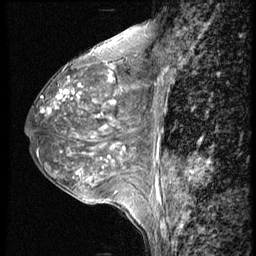
Breast MRI (dynamic contrast-enhanced), one sagittal slice; slice 22 of 56 in the series (ordered by position); 4 images stored at this slice position (order not interpretable as contrast timing); 1.5 T; TE 4.2 ms, TR 9 ms; 2.5 mm slice thickness; 256 × 256 image matrix, field of view 180 × 180 mm. Patient: female, 50 years. Case-level facts recorded for this patient, not image findings: setting: breast cancer imaged before/during neoadjuvant chemotherapy; receptor status: triple-negative.
Structures marked on this image (semi-automatic segmentation, software-assisted and operator-edited):
- analysis volume of interest (the breast-tissue region the enhancement analysis was run in; not a lesion): bounding box (x1, y1, x2, y2) in pixels: (24, 46, 148, 188)
- tumour enhancement mask (voxels above the 140 % enhancement threshold inside the analysis volume of interest): (42, 86, 125, 151)